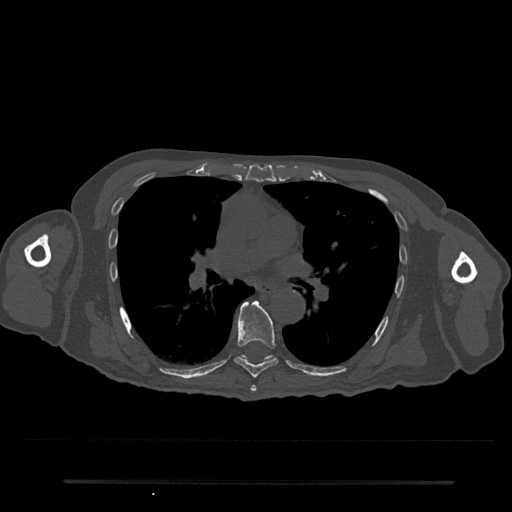
CT including the spine, one axial slice. Position 472 of 797 along the scan axis. Reconstruction kernel Br40s/3. 120 kVp. Bone window (W 1800 / L 400 HU). 0.5 mm slice thickness. 512 × 512 image matrix. Male patient, age 74 years. Case-level facts recorded for this patient, not image findings: primary cancer: prostate.
Annotated regions visible in this slice (semi-automatically segmented with operator editing):
- T6 vertebra: bounding box (x1, y1, x2, y2) in pixels: (250, 385, 257, 392)
- T7 vertebra: (234, 301, 279, 378)
- T8 vertebra: (241, 355, 274, 362)